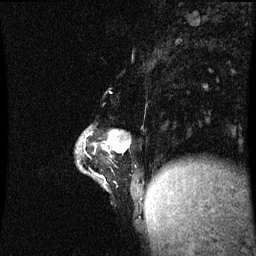
Breast MRI (dynamic contrast-enhanced), one sagittal slice. Position 18 of 60 along the scan axis. Dynamic contrast-enhanced series, image 2 of 3 at this slice position (ordered by acquisition). 1.5 T. TE 4.2 ms, TR 8.9 ms. 256 × 256 image matrix. Patient: female, 47 years. From the clinical record (not read from this slice): setting: breast cancer imaged before/during neoadjuvant chemotherapy; receptor status: HR-positive, HER2-negative.
Outlined on this slice (semi-automatically segmented with operator editing):
- analysis volume of interest (the breast-tissue region the enhancement analysis was run in; not a lesion): box from (x=78, y=128) to (x=146, y=199) px
- tumour enhancement mask (voxels above the 70 % enhancement threshold inside the analysis volume of interest): (x=96, y=134)–(x=130, y=175)